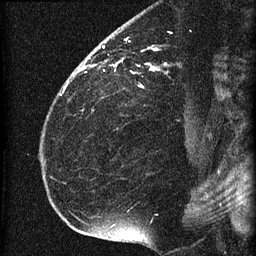
Breast MRI (dynamic contrast-enhanced), one sagittal slice. Slice 45 of 60 in the series (ordered by position). Dynamic contrast-enhanced series, image 2 of 4 at this slice position (ordered by acquisition). 1.5 T. TE 4.2 ms, TR 22.7 ms. 1.5 mm slice thickness. 256 × 256 image matrix, field of view 180 × 180 mm. Patient: female, 35 years. From the clinical record (not read from this slice): setting: breast cancer imaged before/during neoadjuvant chemotherapy; receptor status: HR-positive, HER2-negative.
Outlined on this slice (semi-automatically segmented with operator editing):
- analysis volume of interest (the breast-tissue region the enhancement analysis was run in; not a lesion): box from (x=69, y=27) to (x=198, y=112) px
- tumour enhancement mask (voxels above the 90 % enhancement threshold inside the analysis volume of interest): (x=81, y=39)–(x=159, y=73)